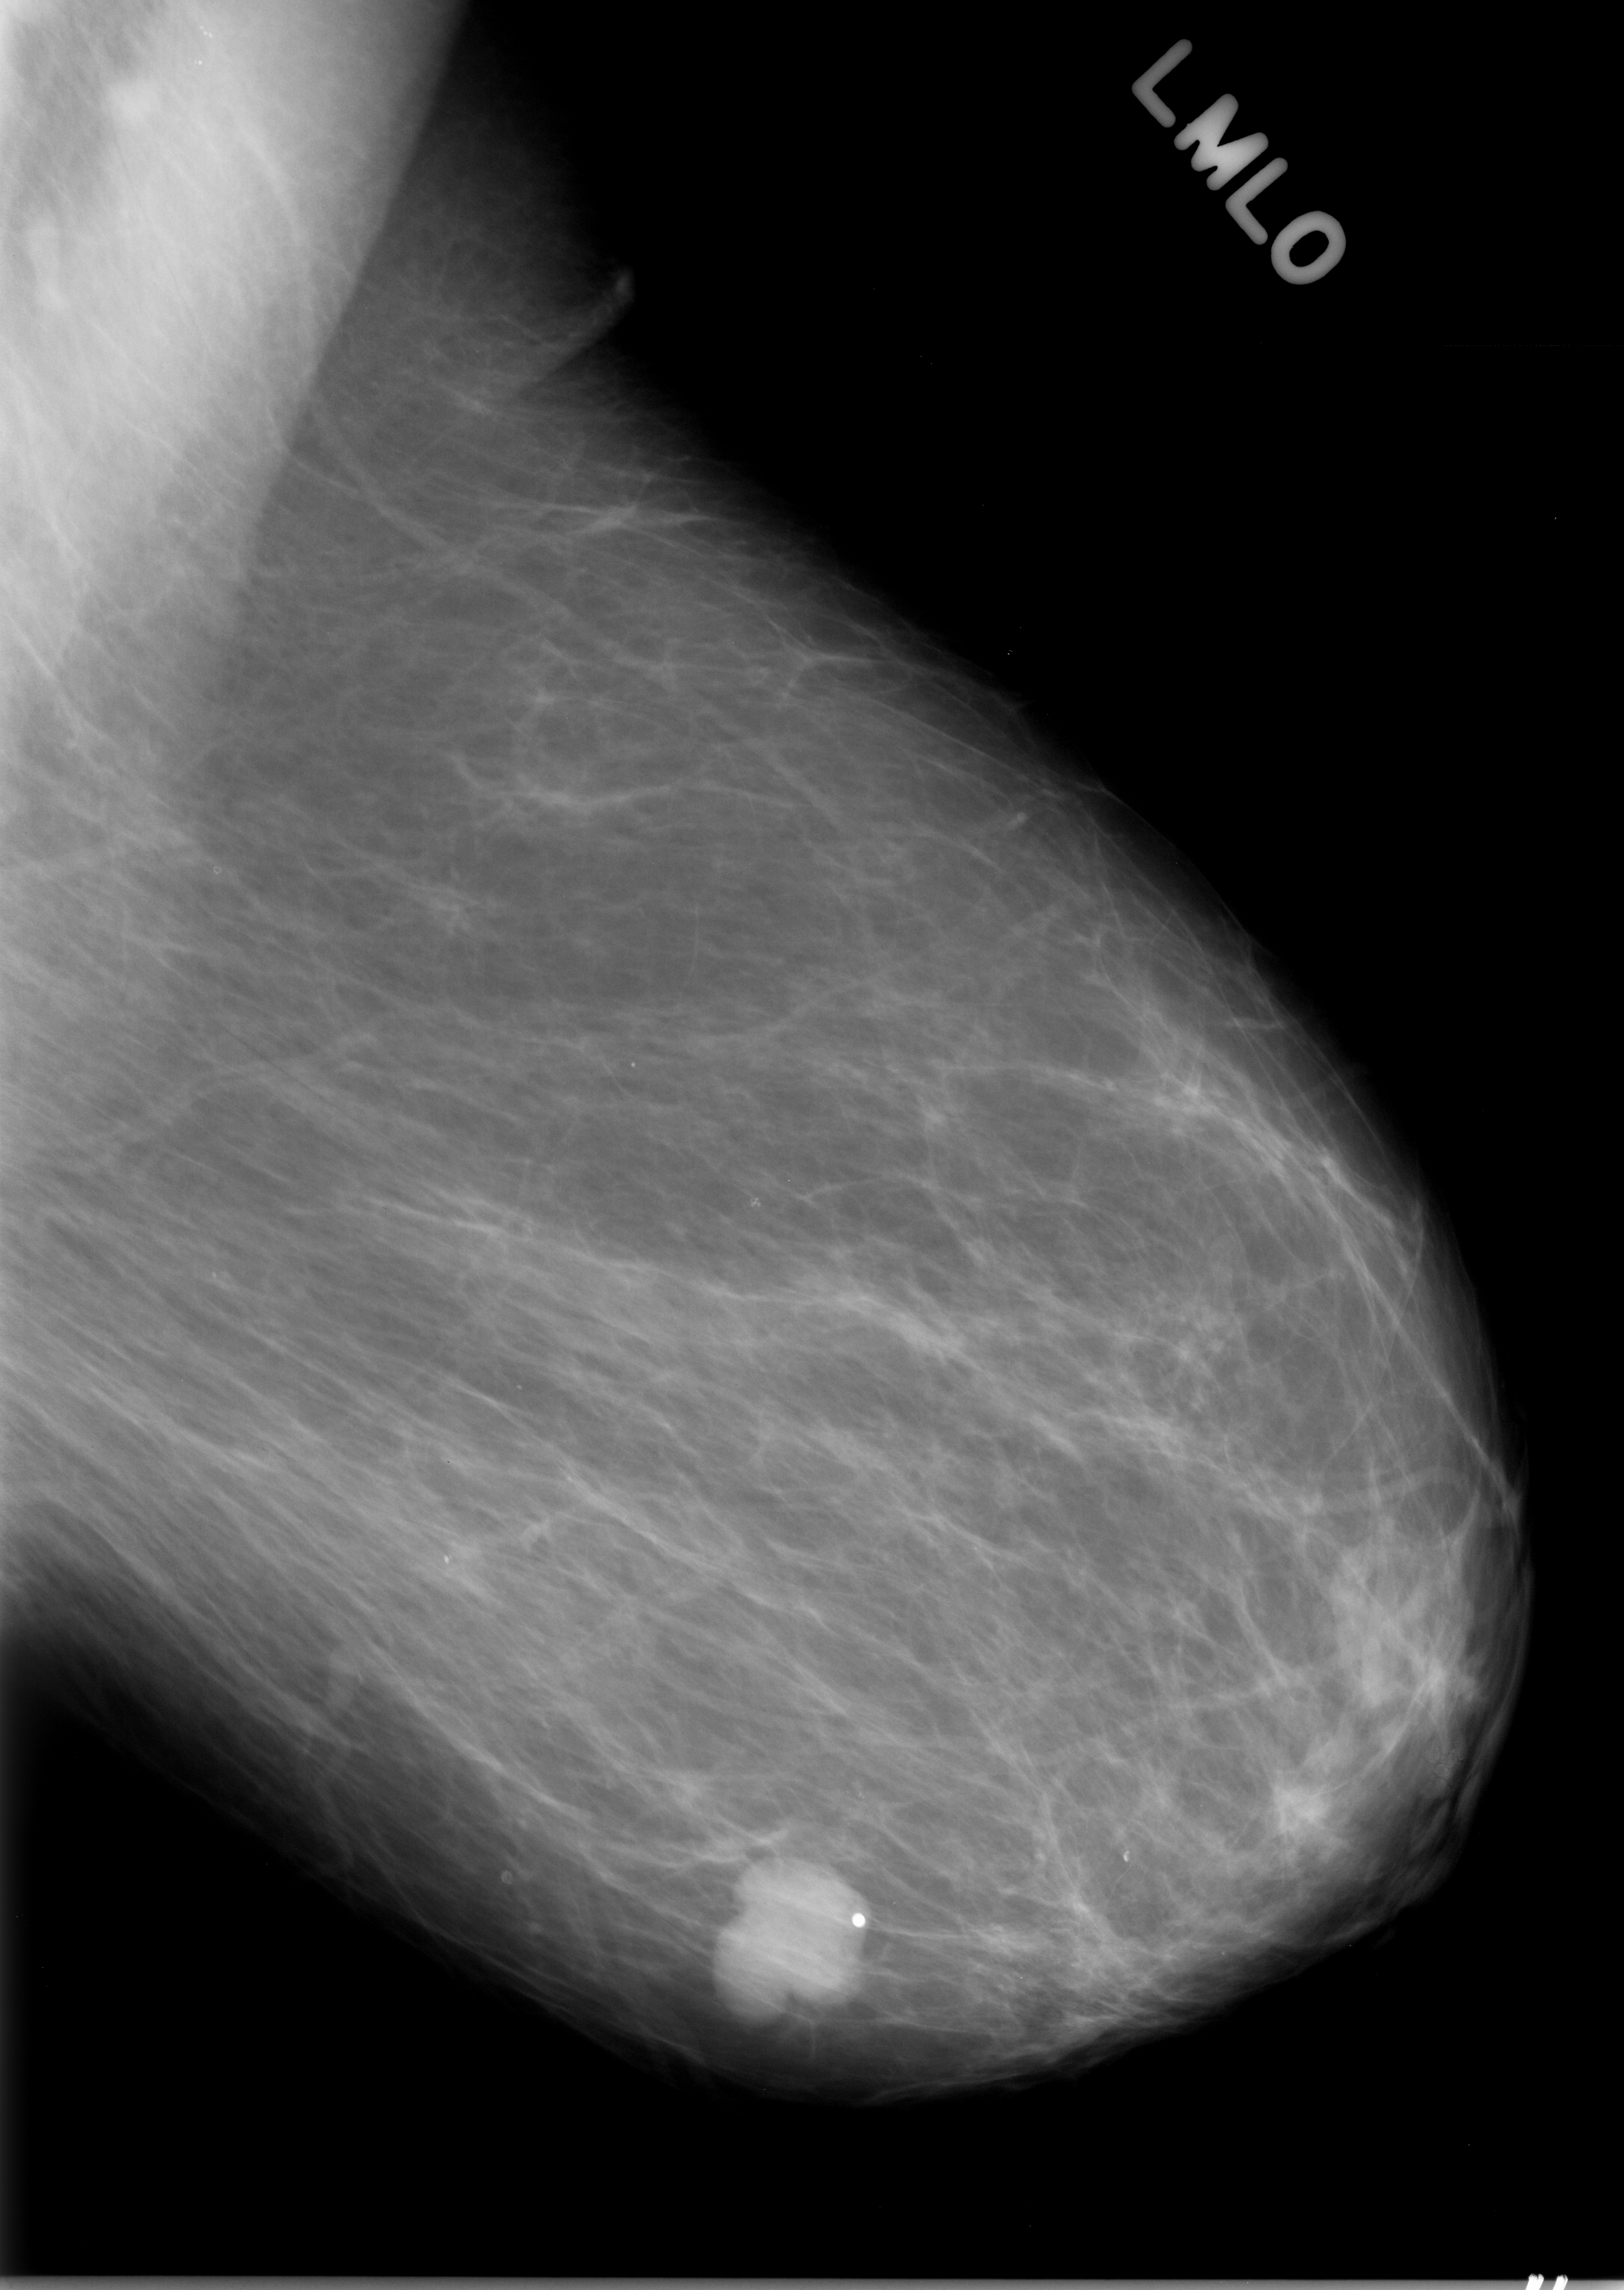
Mammogram (digitized film); left breast; mediolateral oblique (MLO) view; BI-RADS breast density category 1 (scale 1–4); 1624 × 2290 image matrix.
Expert-marked regions of interest on this film, with their recorded descriptors:
- mass, shape lobulated, margins circumscribed; BI-RADS assessment category 5; subtlety rating 5 on a 1 (subtle) to 5 (obvious) scale; pathology (as recorded): malignant: box from (x=703, y=1848) to (x=858, y=2032) px